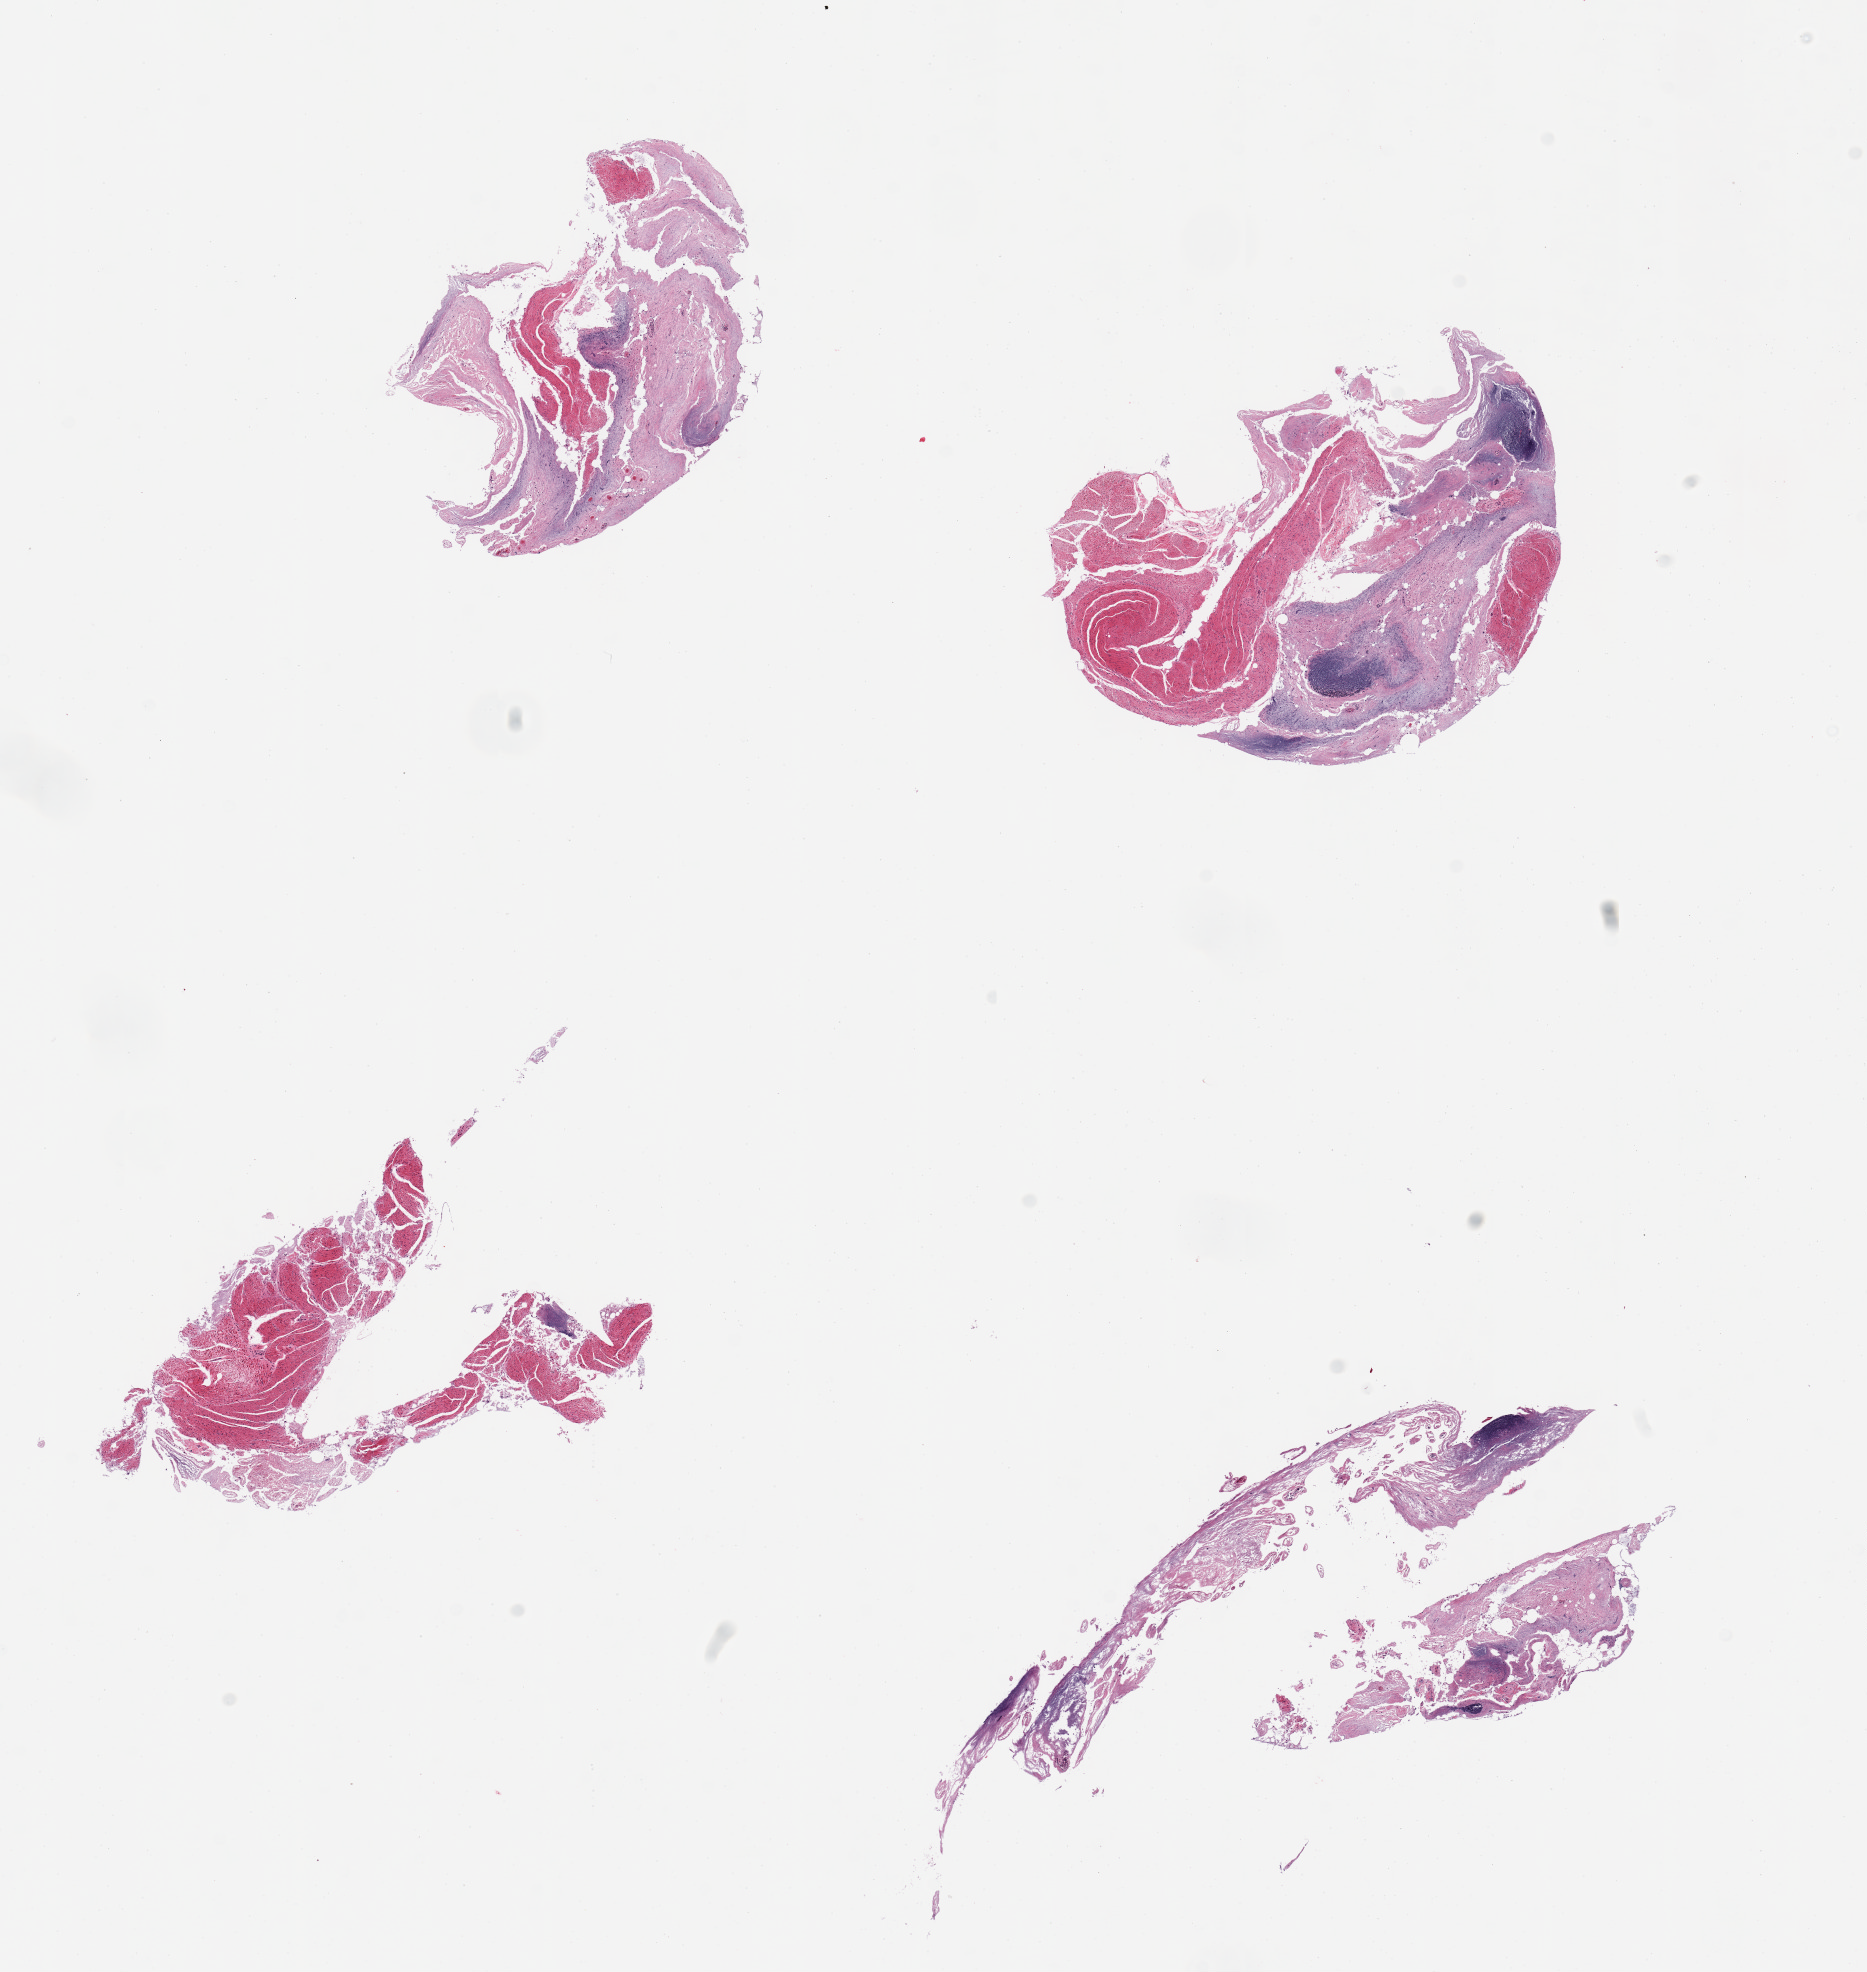
Whole-slide image, H&E stain, whole scanned area (about 14.8 x 15.6 mm) shown as a low-resolution overview, PAXgene-fixed, paraffin-embedded tissue, sampled site (target tissue): ileum, donor tissue sample.
* review note (as recorded): 4 pieces, severely autolyzed mucosa with focal prominent lymphoid tissue and fragments of muscularis (not target)